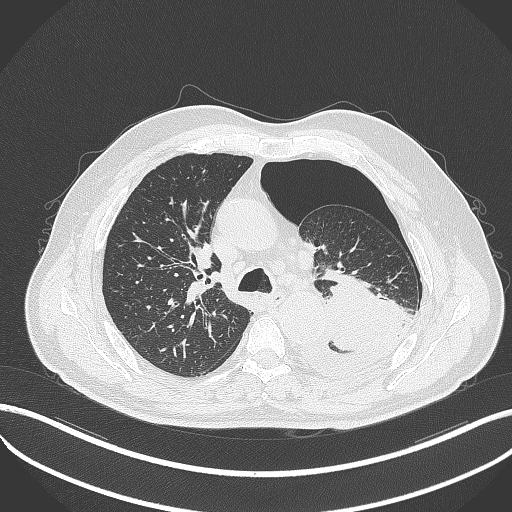
Chest CT, one axial slice. 120 kVp. Lung window (W 1500 / L -600 HU). 1 mm slice thickness. 512 × 512 image matrix. Patient: male, 76 years. From the clinical record (not read from this slice): clinical TNM (as recorded): T3 N0 M1b.
Outlined on this slice (bounding box drawn by a radiologist):
- lung tumour (recorded histology: adenocarcinoma): box from (x=322, y=267) to (x=407, y=350) px